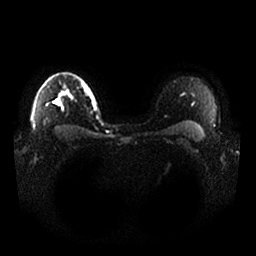
Breast MRI, one axial slice. Position 23 of 25 along the scan axis. Diffusion-weighted series; image 2 of 4 stored at this slice position (different b-values; order by instance number). 1.5 T. 4 mm slice thickness. 256 × 256 image matrix, field of view 370 × 370 mm. Female patient.
Outlined on this slice (expert manual segmentation):
- tumour on diffusion-weighted imaging: box from (x=55, y=101) to (x=60, y=104) px